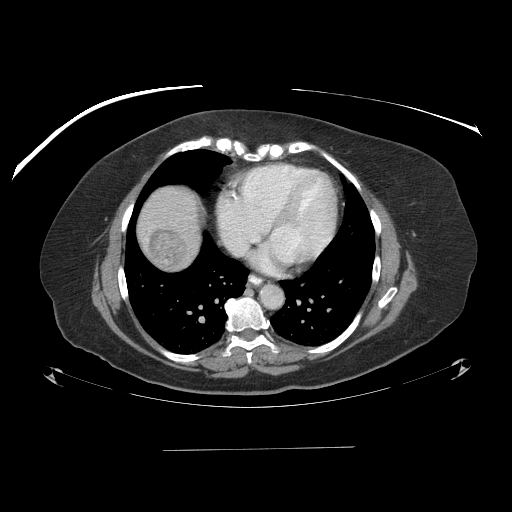
Contrast-enhanced abdominal CT (liver protocol), one axial slice; position 85 of 103 along the scan axis; 120 kVp; one of 2 acquisitions stored at this slice position; soft-tissue window (W 400 / L 40 HU); 2.5 mm slice thickness; 512 × 512 image matrix, field of view 500 × 500 mm. Case-level facts recorded for this patient, not image findings: diagnosis: hepatocellular carcinoma (patient treated with transarterial chemoembolisation; whether this scan precedes or follows treatment is not stated here); TNM stage (as recorded): Stage-IIIA; Child-Pugh class: A; tumour nodularity: multinodular.
Outlined on this slice (semi-automatically segmented with operator editing):
- liver parenchyma outside the tumour (the mass and vessels are separate outlines, so this box may not span the whole liver): box from (x=136, y=186) to (x=200, y=268) px
- mass: (x=147, y=229)–(x=188, y=267)